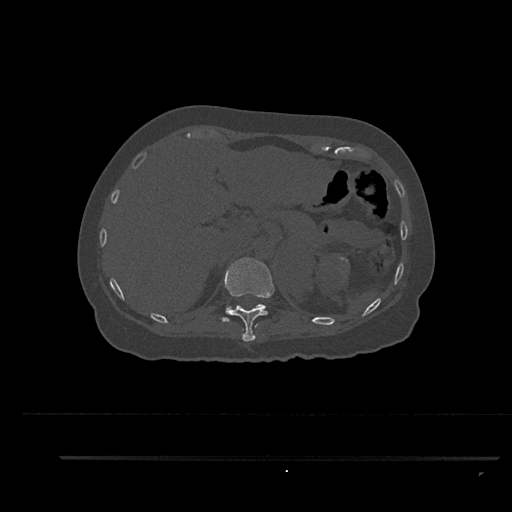
CT including the spine, one axial slice; slice 304 of 797 in the series (ordered by position); 120 kVp; bone window (W 1800 / L 400 HU); 0.5 mm slice thickness; 512 × 512 image matrix, field of view 408 × 408 mm. Female patient, age 44 years. Case-level facts recorded for this patient, not image findings: primary cancer: renal.
Annotated regions visible in this slice (semi-automatic segmentation, software-assisted and operator-edited):
- T11 vertebra: bounding box <224,257,275,342> (left, top, right, bottom; pixels)
- T12 vertebra: <221,304,265,322>